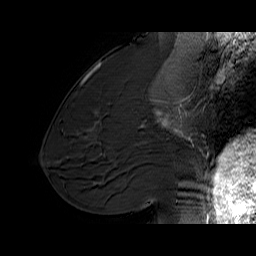
Breast MRI (dynamic contrast-enhanced), one sagittal slice. Slice 31 of 60 in the series (ordered by position). Dynamic contrast-enhanced series, time point 2 of 6 at this slice position (early post-contrast). 1.5 T. TE 6.1 ms, TR 32.9 ms. 4 mm slice thickness. 256 × 256 image matrix. Female patient. From the clinical record (not read from this slice): setting: breast cancer imaged before/during neoadjuvant chemotherapy; receptor status: HER2-positive.
Structures marked on this image (semi-automatically segmented with operator editing):
- analysis volume of interest (the breast-tissue region the enhancement analysis was run in; not a lesion): bounding box [x1, y1, x2, y2] px = [127, 95, 194, 165]
- tumour enhancement mask (voxels above the 100 % enhancement threshold inside the analysis volume of interest): [141, 97, 190, 140]